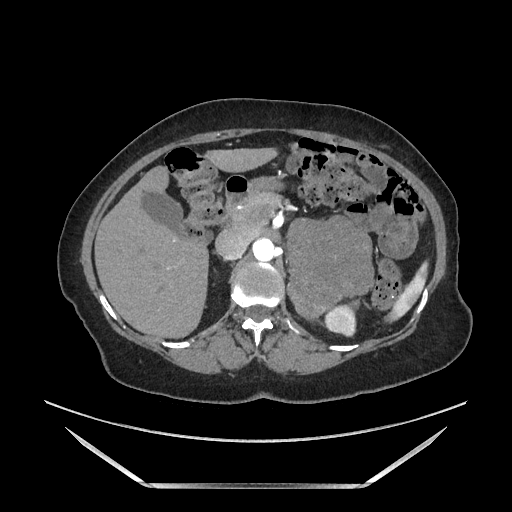
Contrast-enhanced abdominal CT, one axial slice; slice 104 of 205 in the series (ordered by position); soft-tissue window (W 400 / L 40 HU); 512 × 512 image matrix, field of view 440 × 440 mm. Female patient. Case-level facts recorded for this patient, not image findings: diagnosis: adrenocortical carcinoma; tumour side: left adrenal; tumour size at pathology: 12.5 cm; Ki-67 index: 39 %; stage (as recorded): 3.
Structures marked on this image (semi-automatic segmentation, software-assisted and operator-edited):
- mass: box from (x=290, y=220) to (x=373, y=316) px